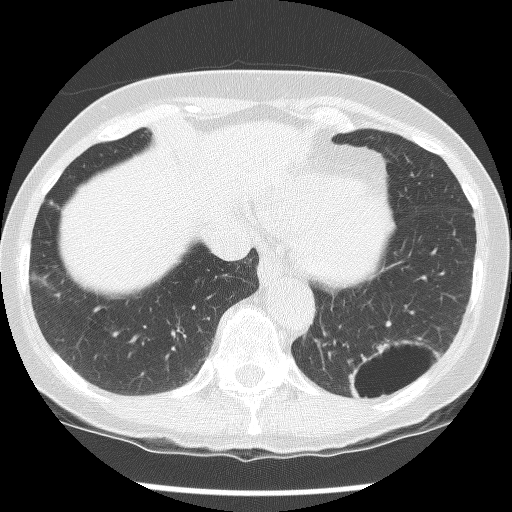
Chest CT (low-dose screening protocol), one axial image; second screening round (one year after baseline); lung window (W 1500 / L -600 HU); 2.5 mm slice thickness; lung (sharp) reconstruction kernel (BONE); slice 99 of 136 in the series. Female, age 61 years at enrolment. Current smoker at enrolment.
Lesion marked by an expert reader, bounding box (x1, y1, x2, y2) in pixels: (329, 316, 439, 413). The screening reader recorded 2 non-calcified nodules or masses ≥4 mm on this exam (left lower lobe, left lower lobe); which of them this box marks is not recorded. Participant outcome: lung cancer diagnosed 585 days after this screen — non-small cell carcinoma, left lower lobe, poorly differentiated (G3), stage IB (AJCC 6th edition), 100 mm at pathology.